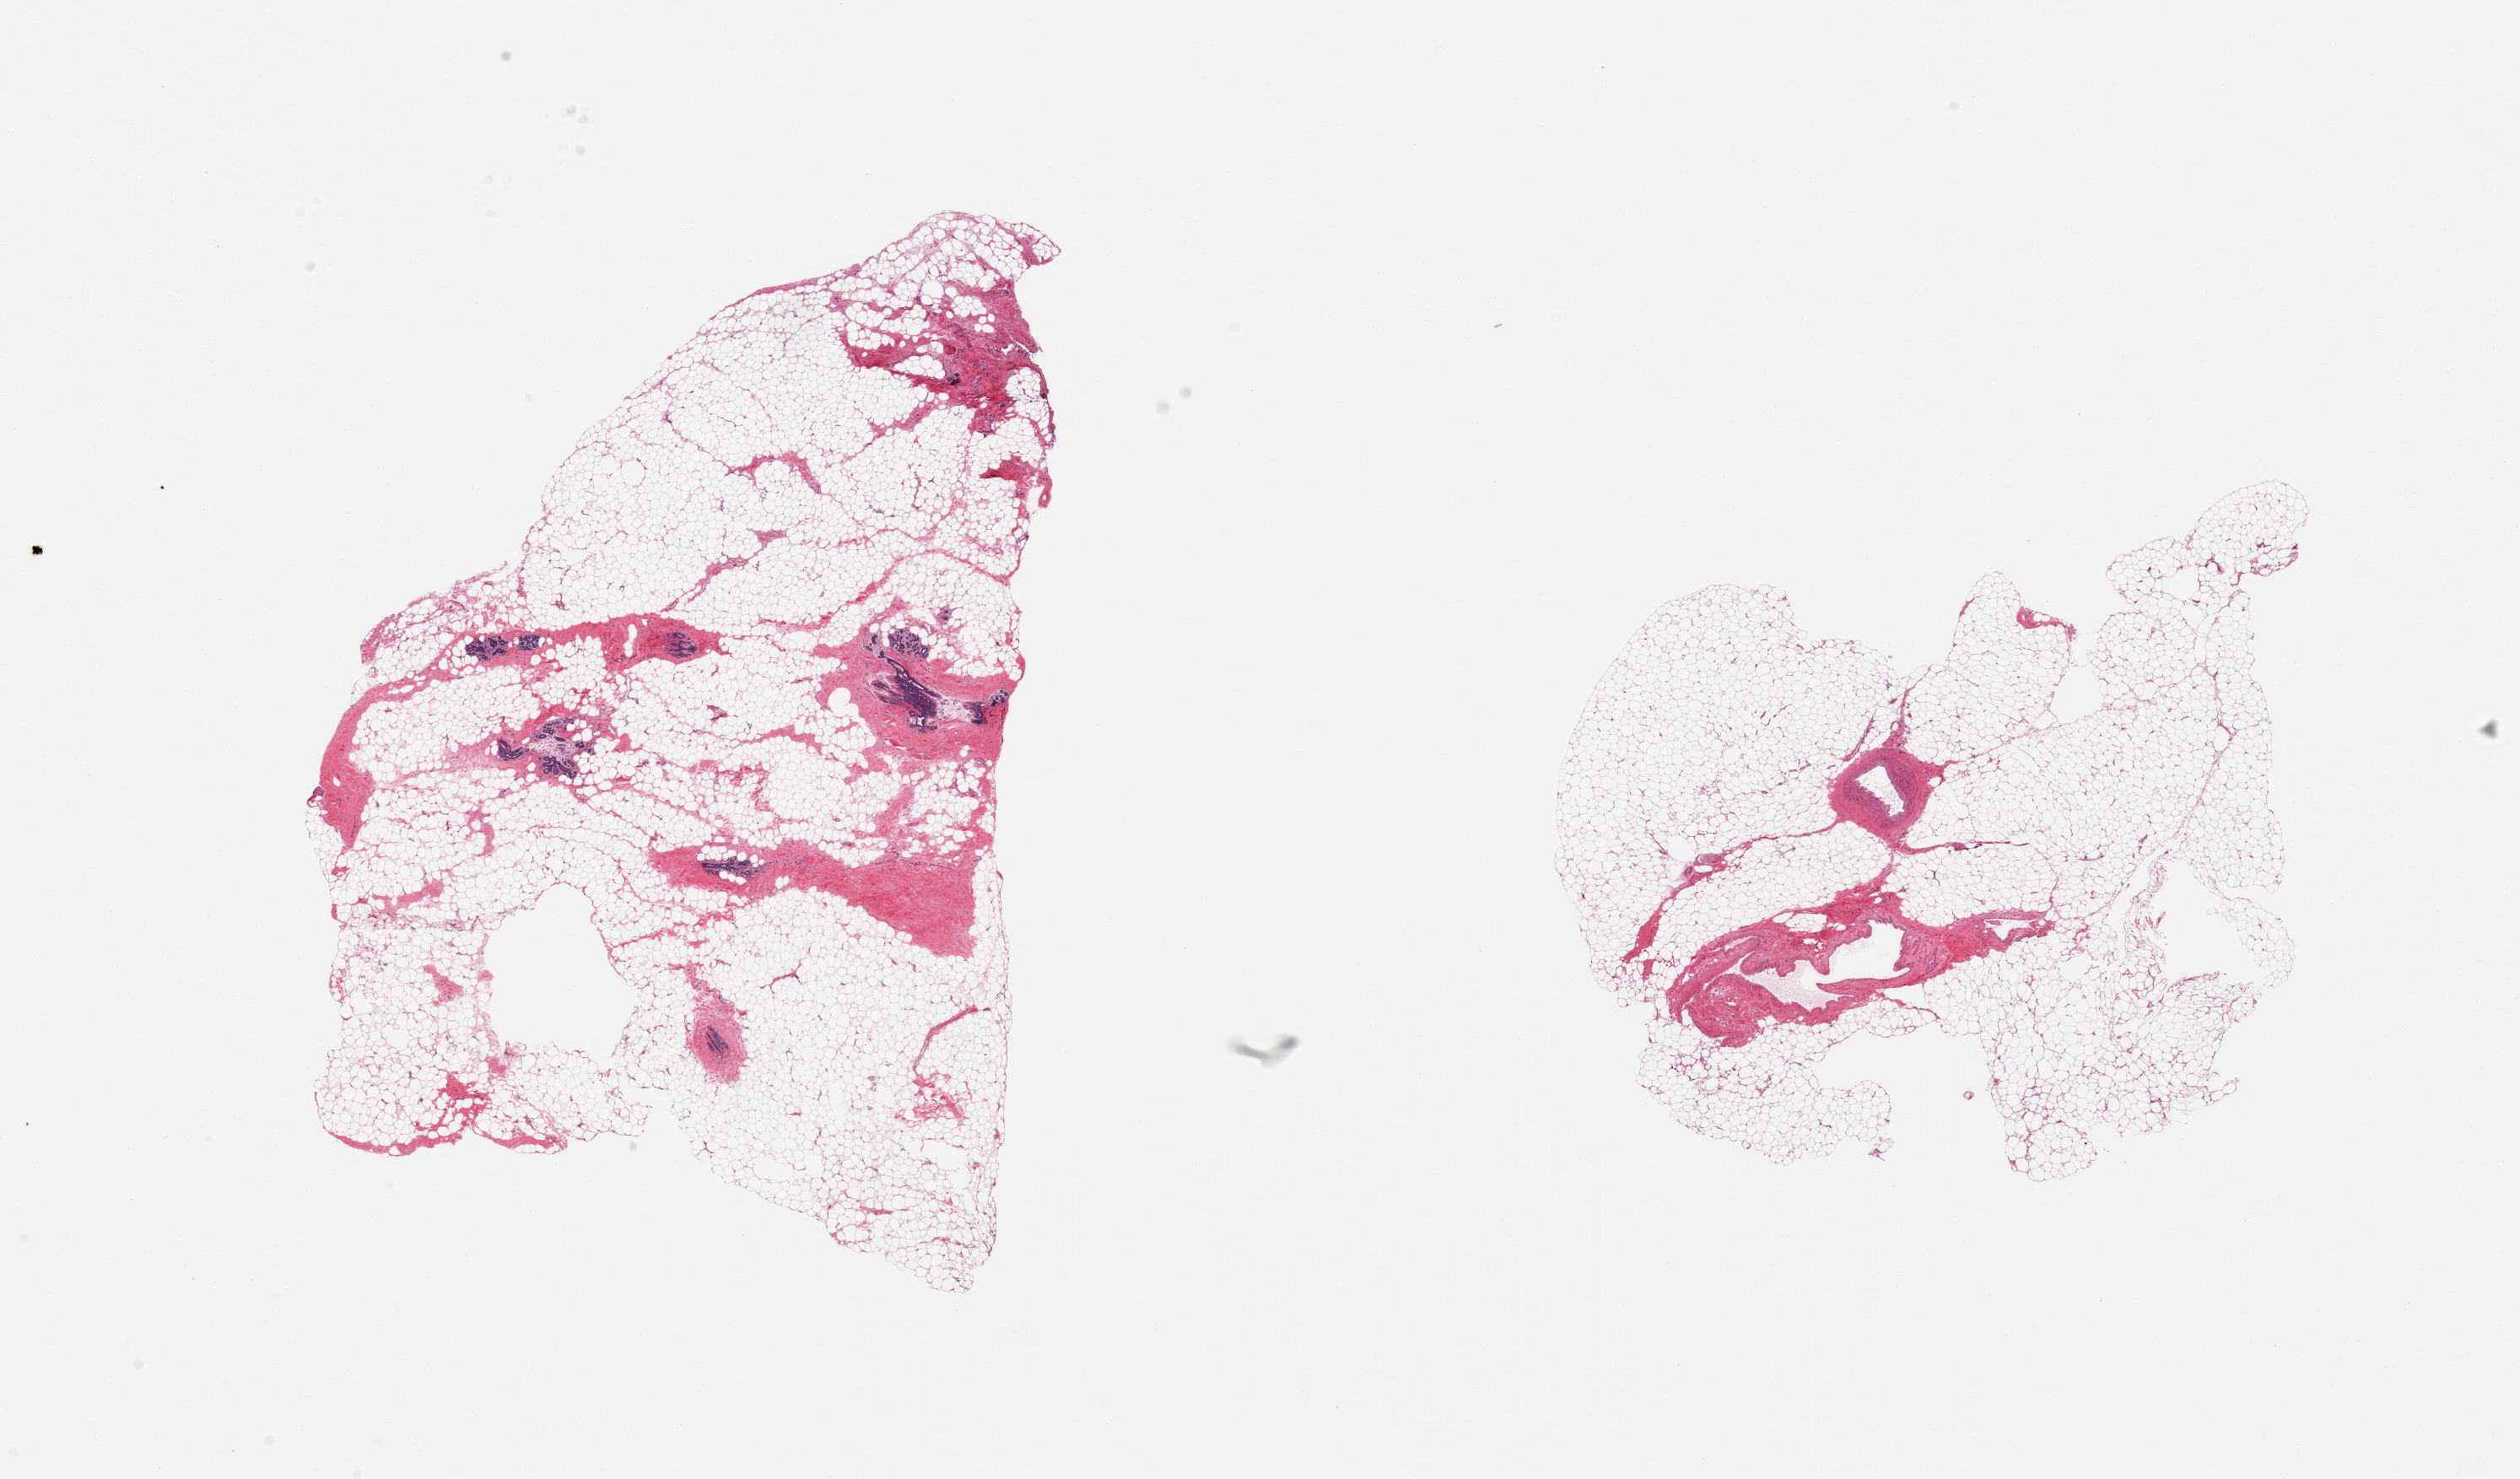
Whole-slide image, H&E stain, a low-resolution overview of the entire scanned area, about 23.6 x 13.9 mm (from a 20x scan). PAXgene-fixed paraffin-embedded (PFPE) section. Sampled site (target tissue): breast. Tissue donor sample. Female donor.
Reviewer comment on this tissue sample: 2 pieces: 1 with atrophic ducts and lobules, 80% fat; other piece is fibroadipose tissue without mammary elements.